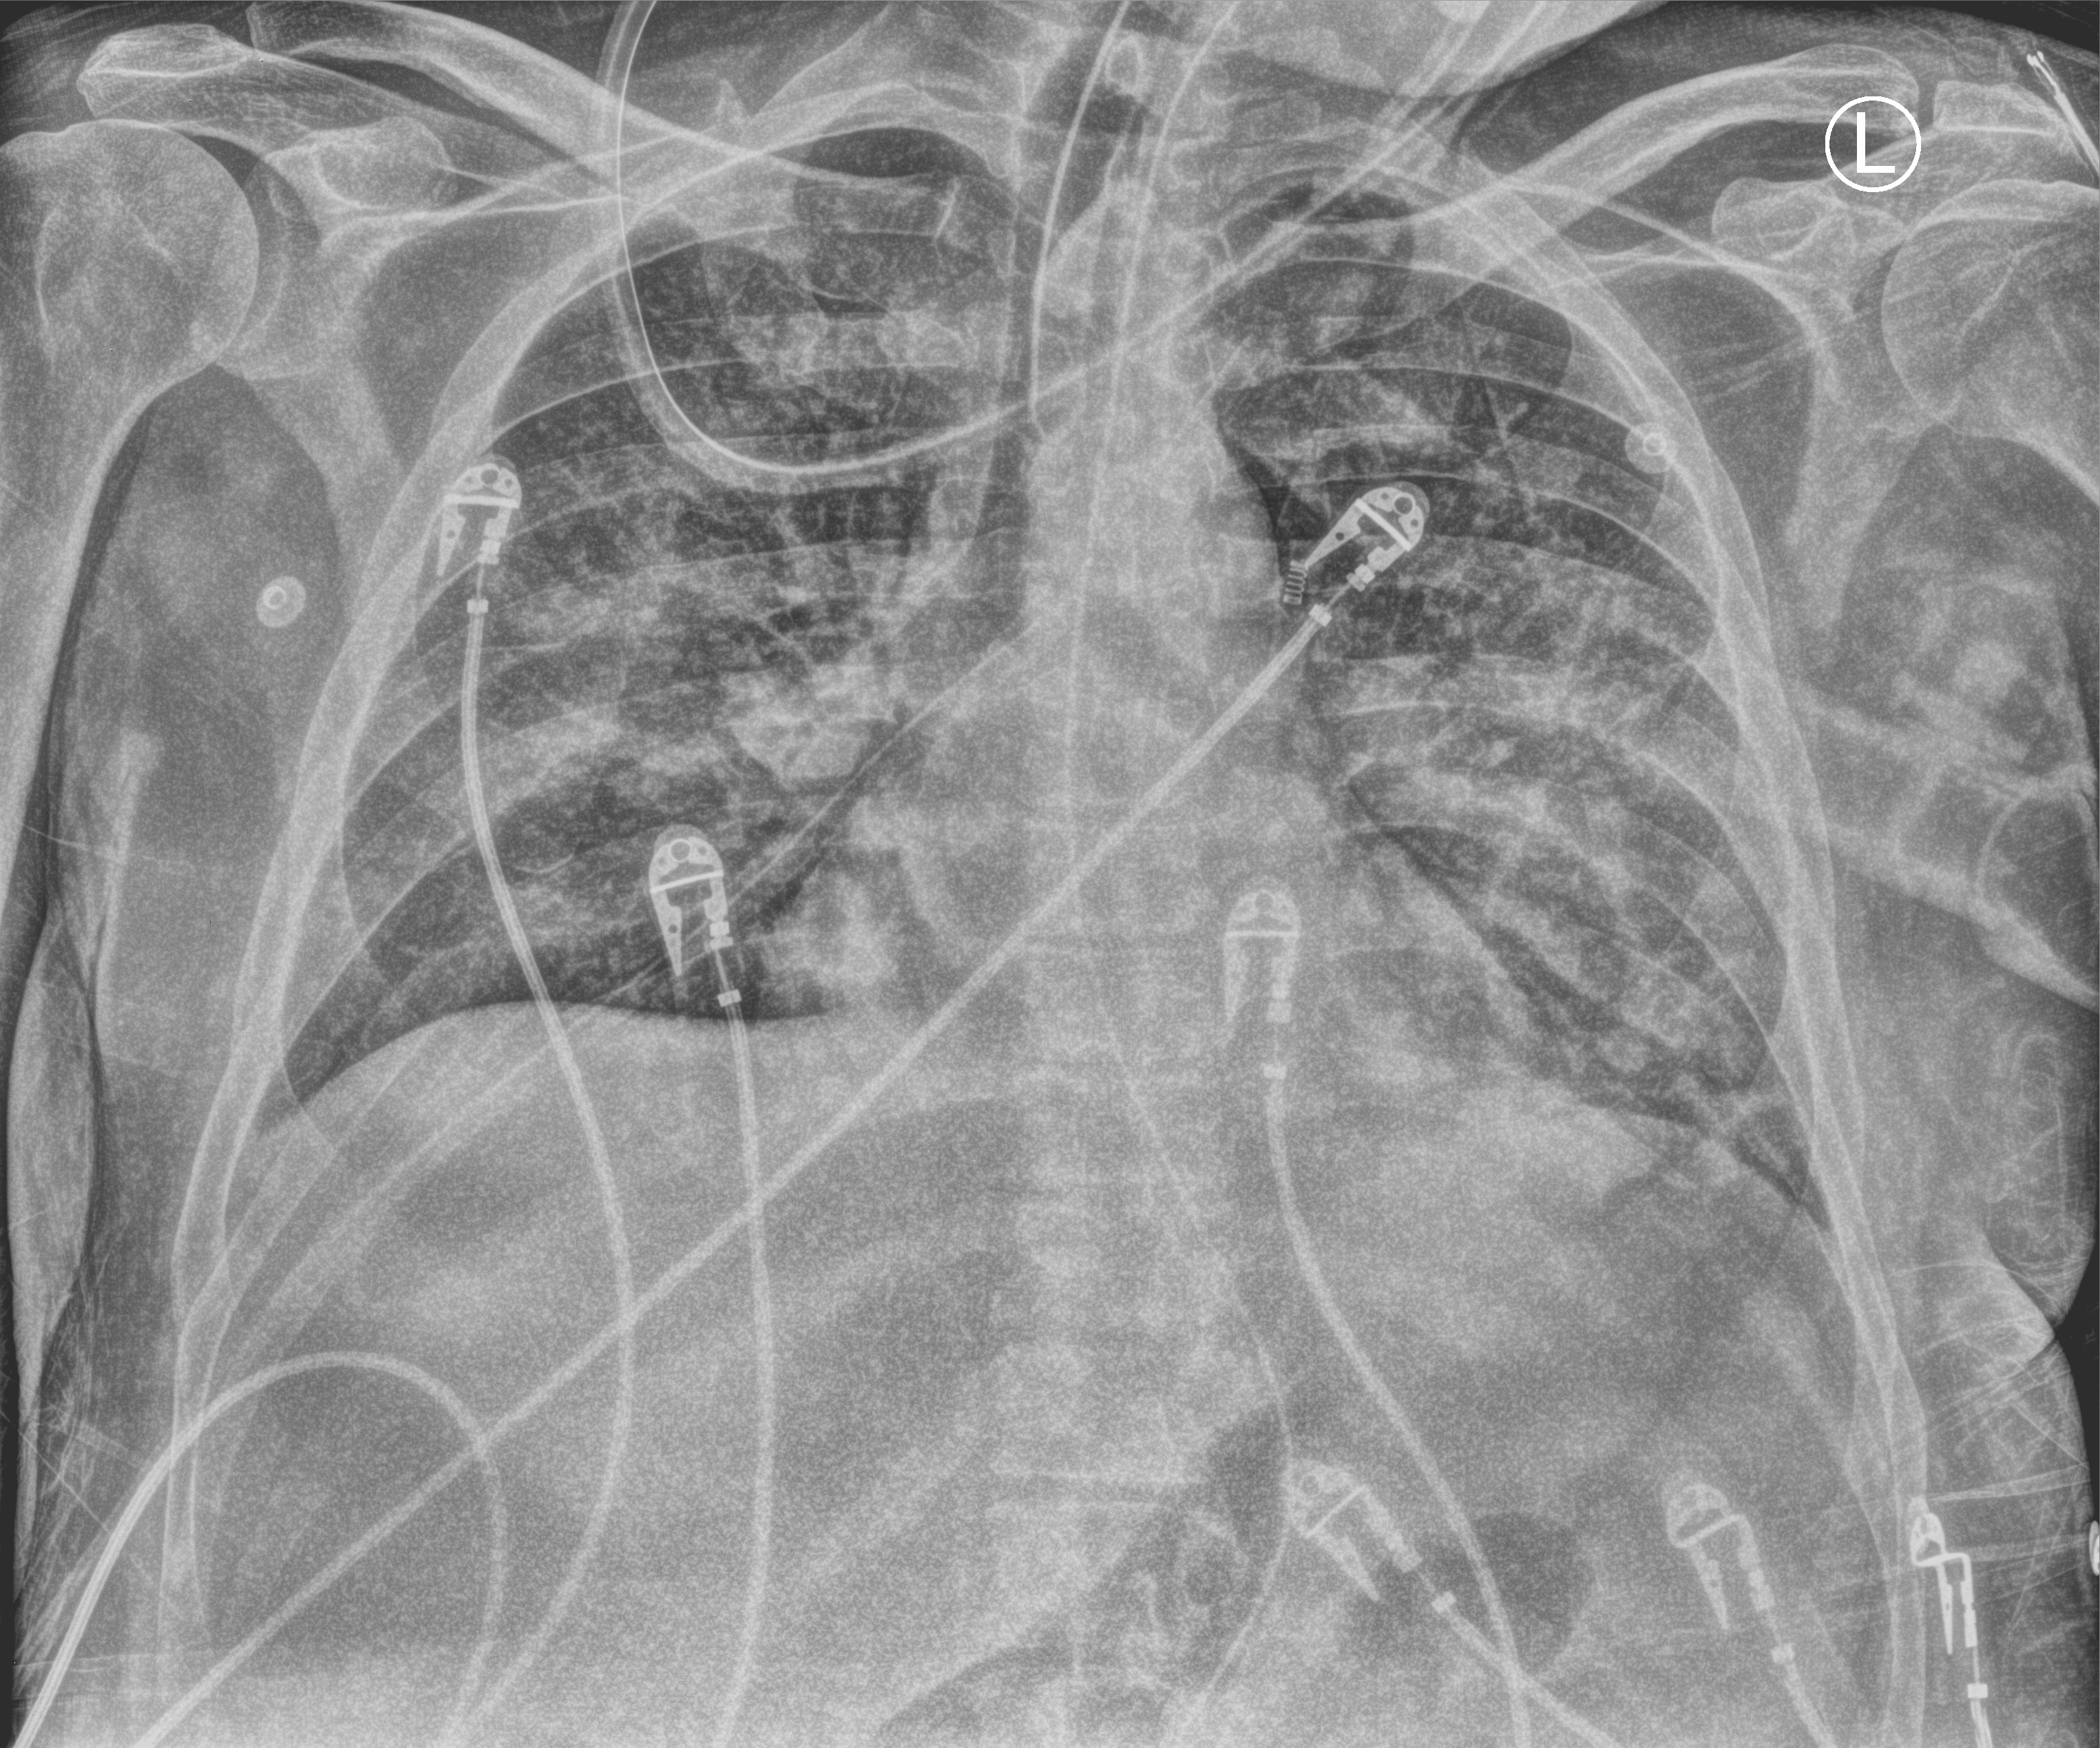
Bedside chest radiograph (computed radiography), anteroposterior (AP) projection. Male patient hospitalised with COVID-19, age 18–59 years.
Hospital-stay facts (about this admission, not read from this image; timing relative to this image not recorded): admitted to intensive care during this hospital stay: yes; mechanically ventilated during this hospital stay: yes; hypertension (admission record): no.